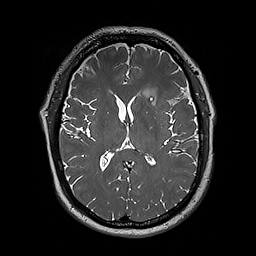
Brain MRI from a brain-tumour surgery series, one axial slice; position 104 of 192 along the scan axis; 1 mm slice thickness; 256 × 256 image matrix. Case-level facts recorded for this patient, not image findings: histopathology: Oligodendroglioma; WHO grade: 3.
Outlined on this slice (expert manual segmentation):
- tumour: bounding box (x1, y1, x2, y2) in pixels: (143, 83, 188, 117)